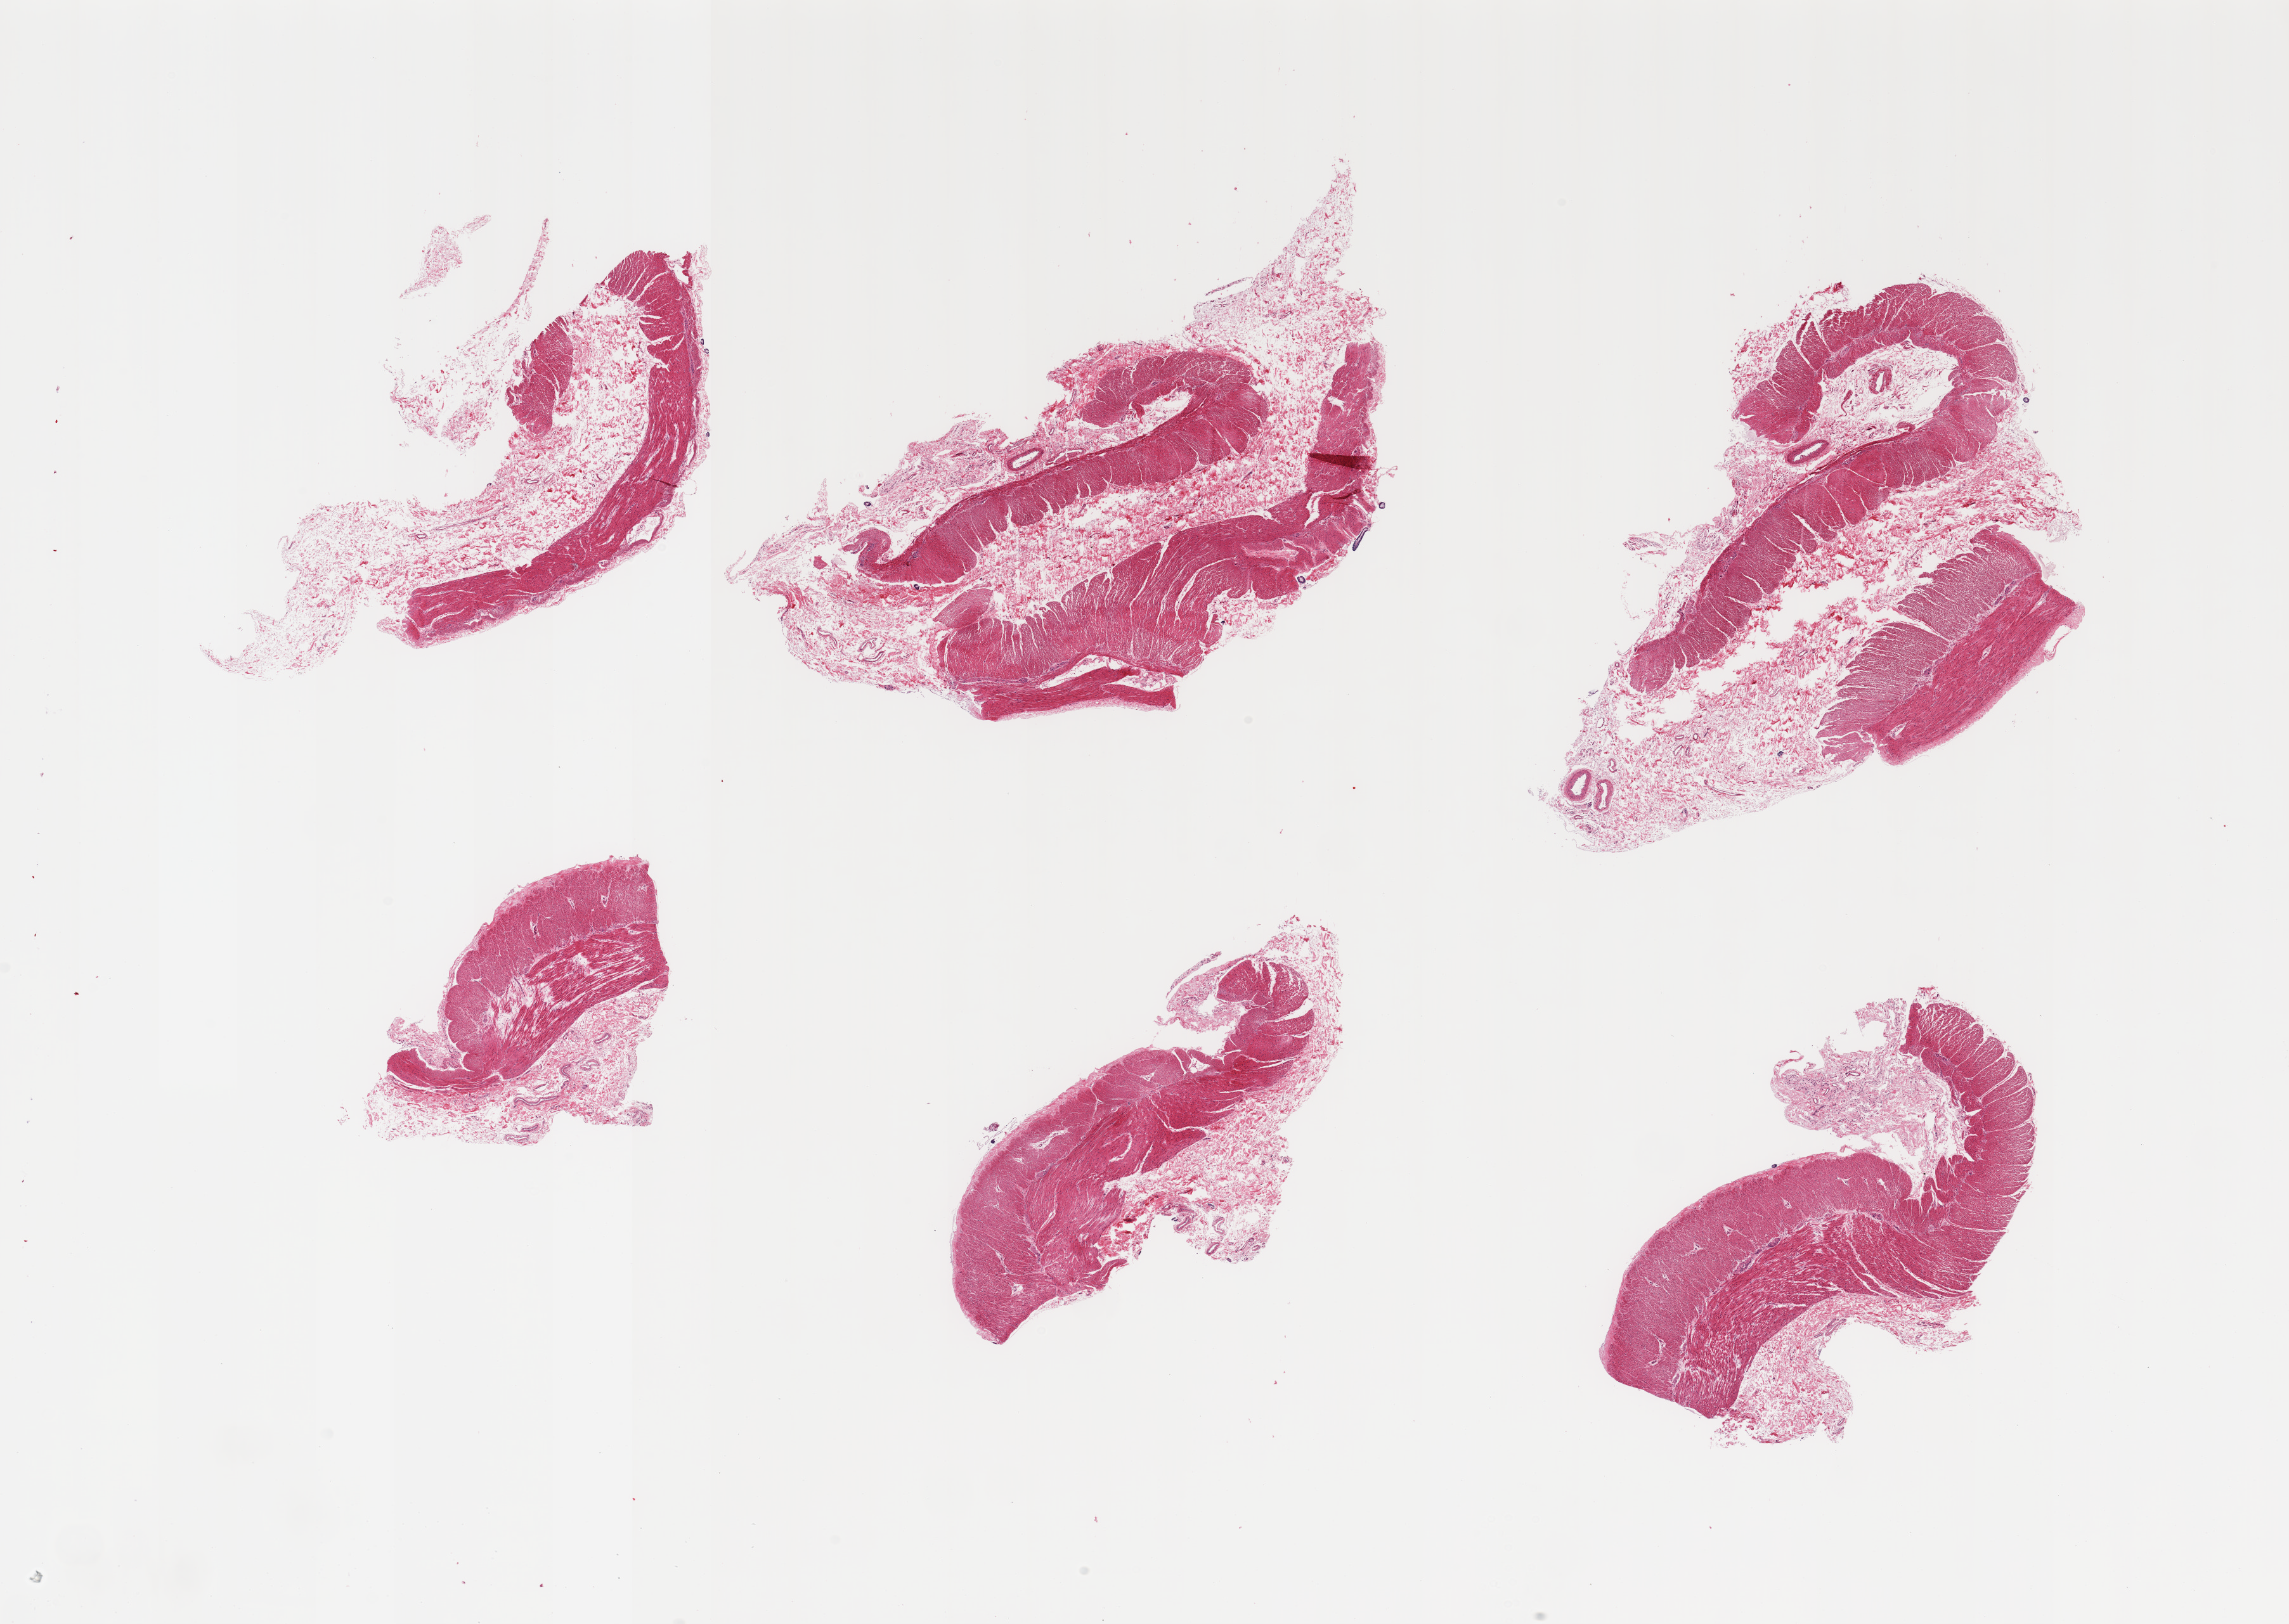
Hematoxylin and eosin (H&E) whole-slide image, low-resolution overview of the scanned area, about 28.5 x 20.3 mm (from a 20x scan). PAXgene-fixed, paraffin-embedded tissue. Sampled site (target tissue): transverse colon. Donor tissue sample. Male donor.
* pathologist's review note for this sample: 6 pieces; muscularis and submucosa, no mucosa (also target)